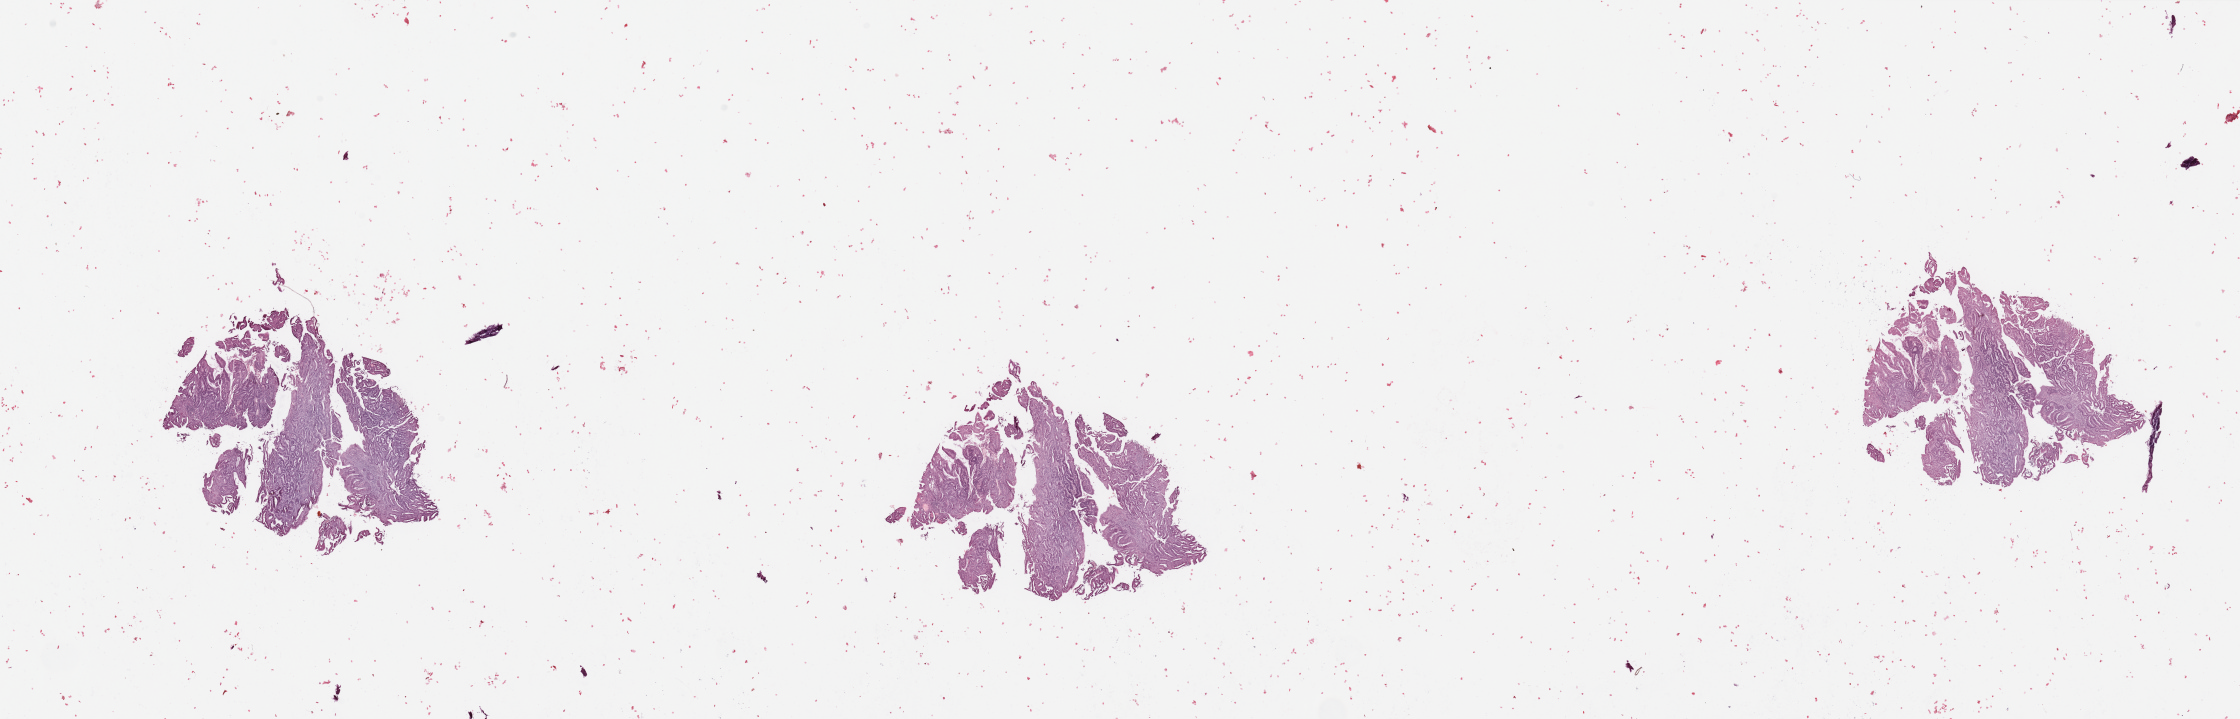
Digitized Hematoxylin and eosin (H&E) stained tissue section (whole slide) — low-resolution overview of the scanned area, about 35.4 x 11.4 mm; uterus, tumour tissue. 72-year-old female patient. Histologic grade: G1 (well differentiated).
• AJCC pathologic stage: I
• diagnosis: Endometrioid adenocarcinoma, NOS